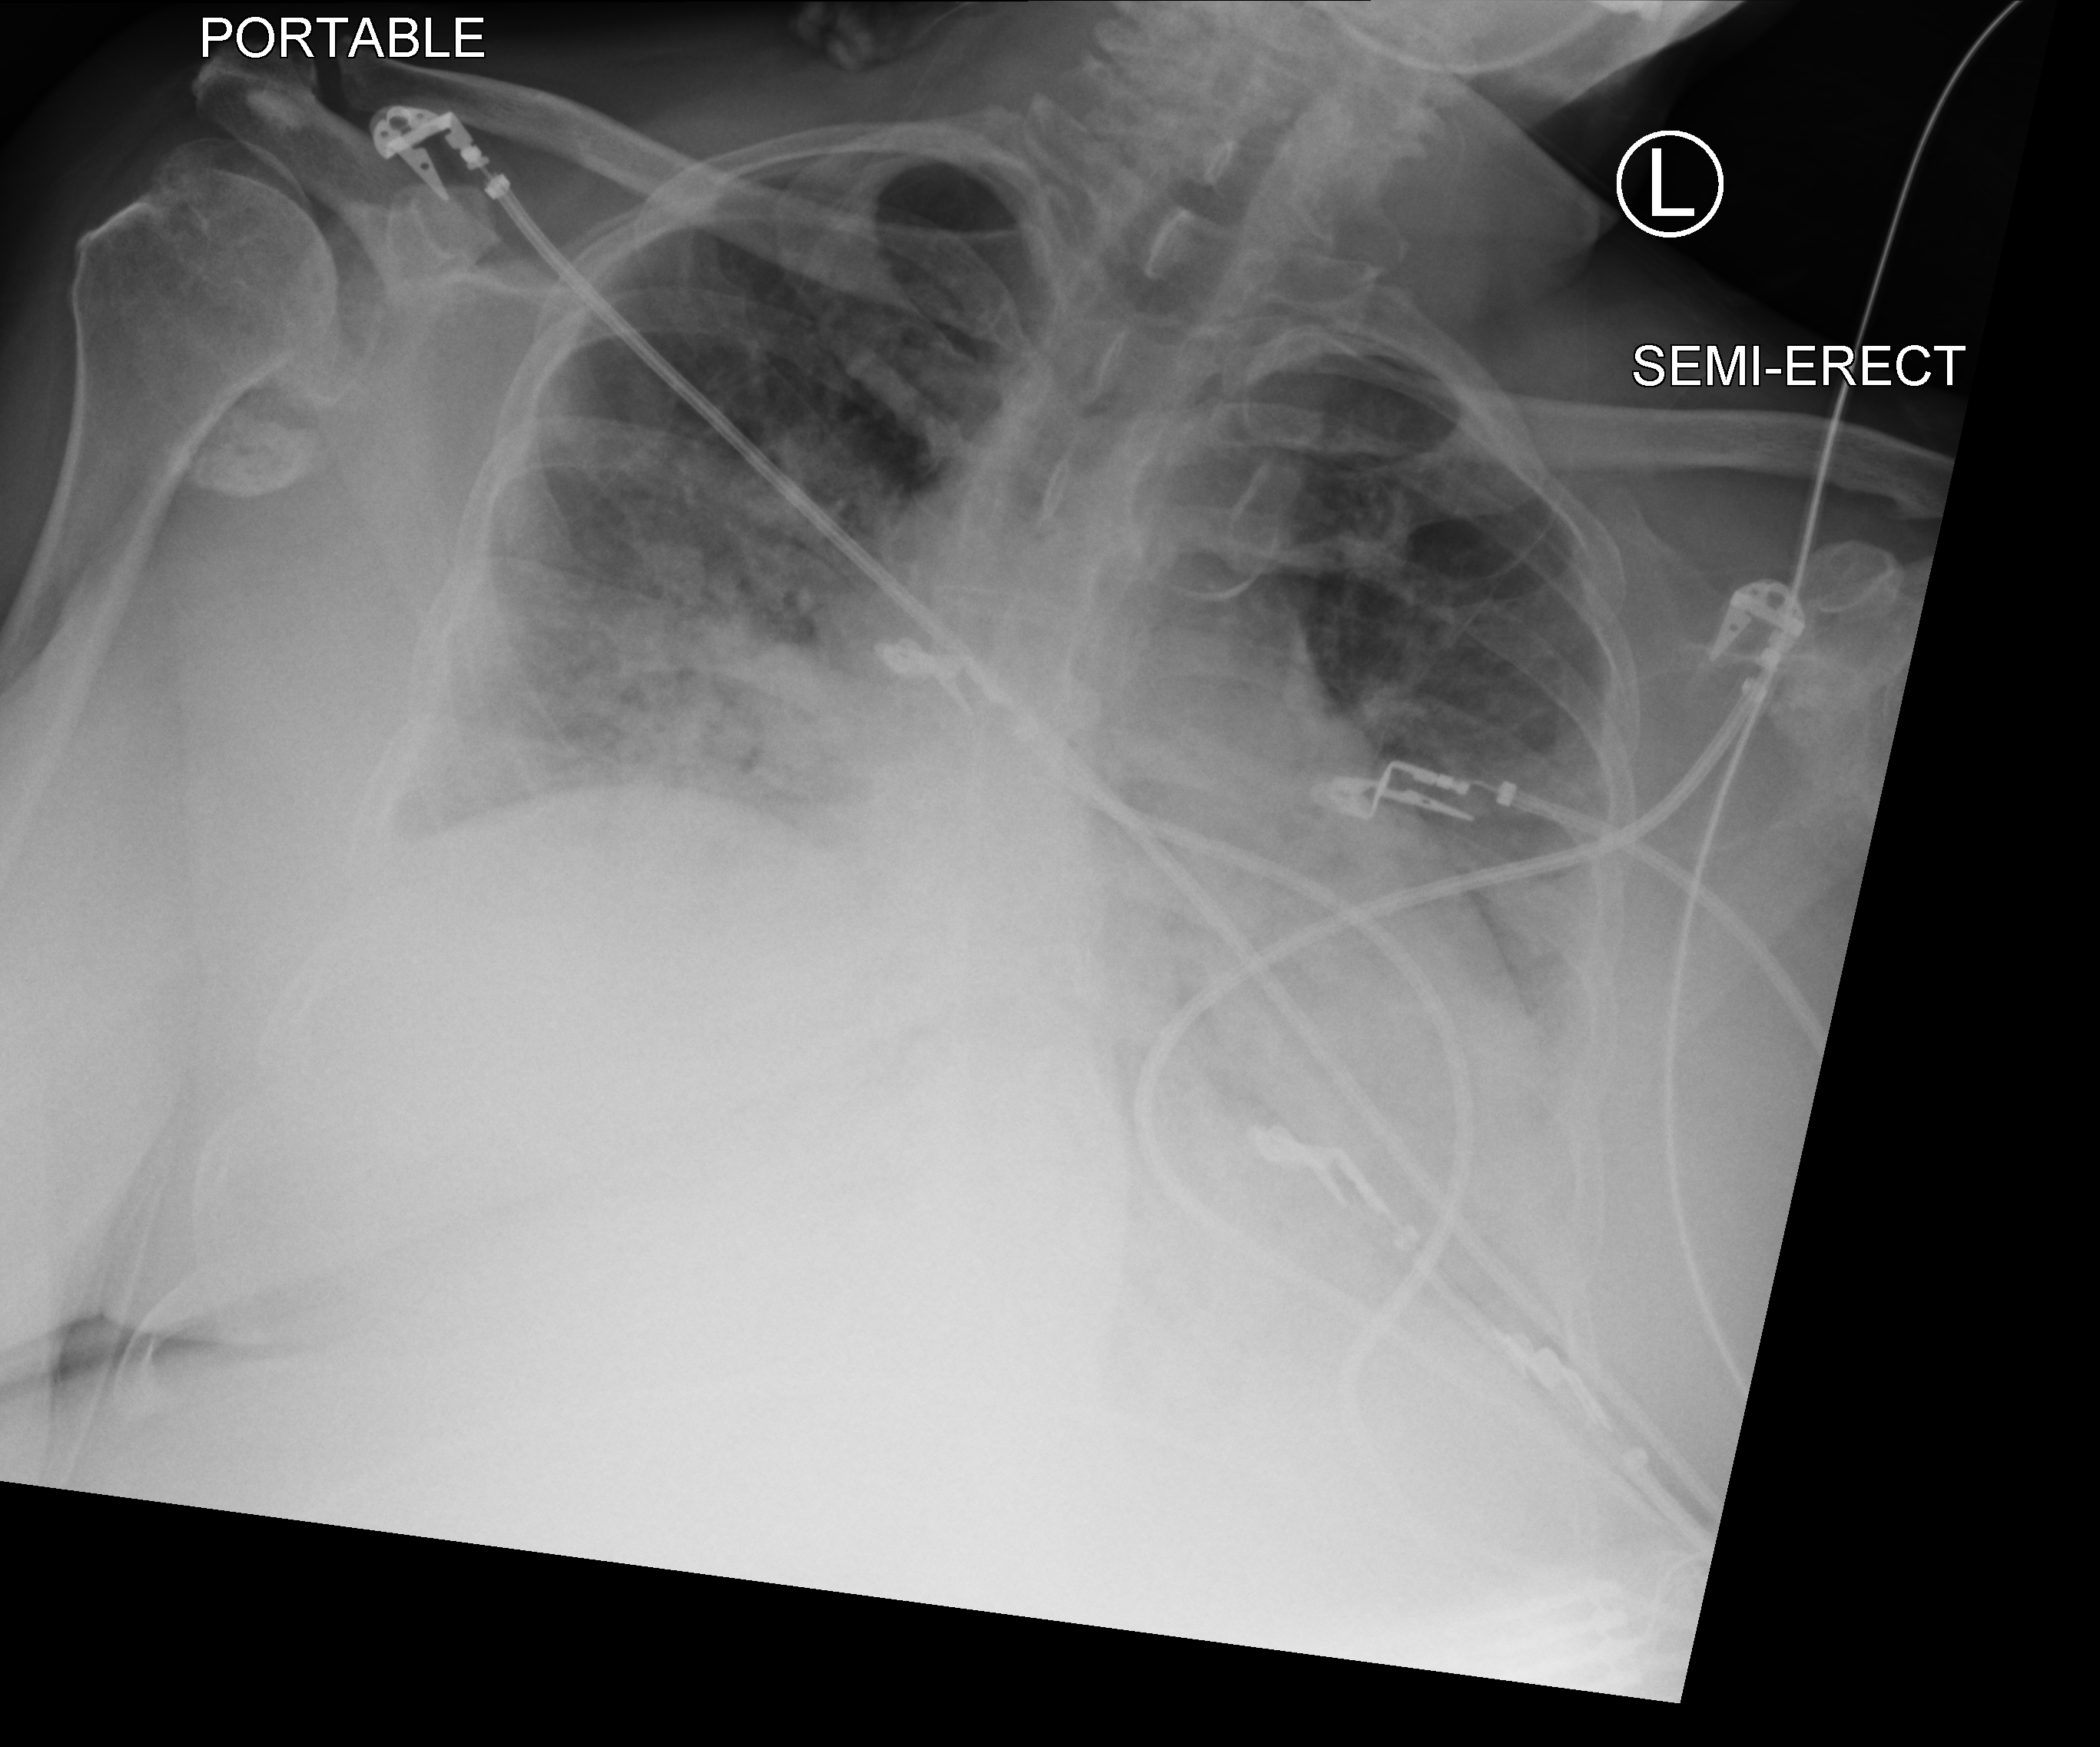
Portable chest radiograph. Patient hospitalised with COVID-19; female, aged 60–74 years.
From the hospital-stay record, not from the radiograph (when in the stay this image was taken is not recorded):
- mechanically ventilated during this hospital stay: yes